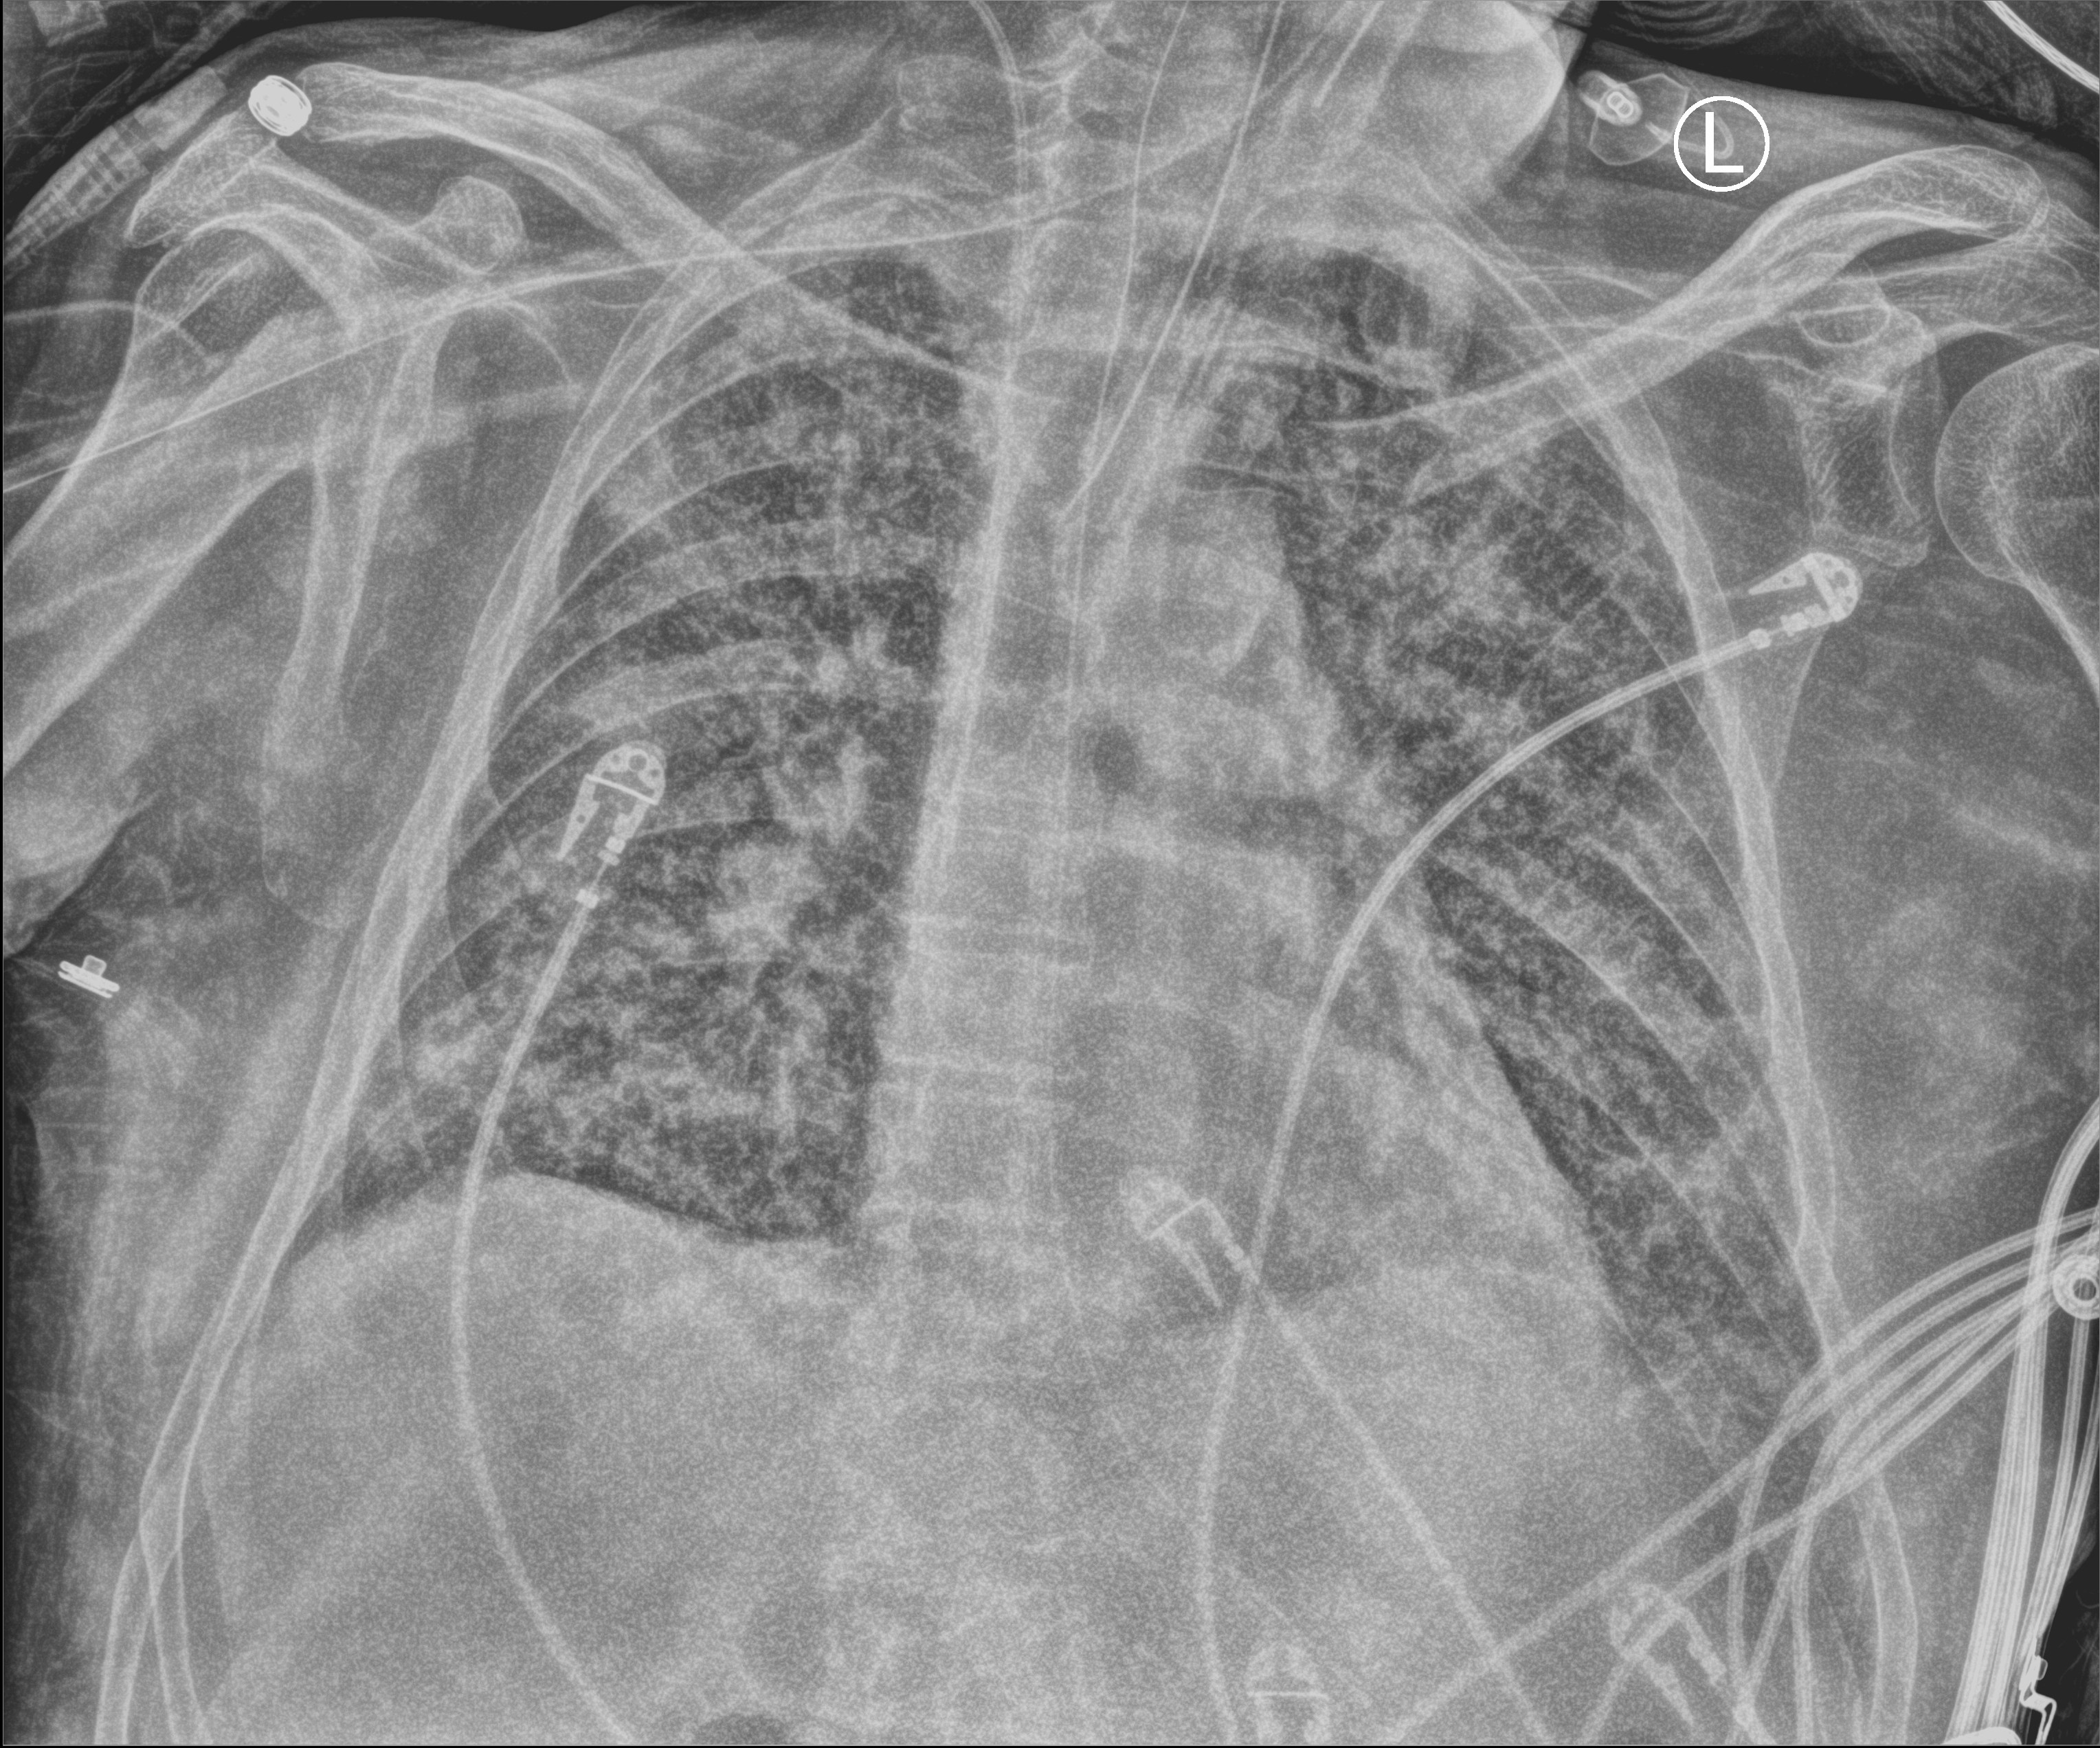
Bedside chest radiograph (computed radiography); anteroposterior (AP) projection. Patient hospitalised with COVID-19; male, aged 60–74 years.
Hospital-stay facts (about this admission, not read from this image; timing relative to this image not recorded):
- mechanically ventilated during this hospital stay: yes
- diabetes (admission record): no
- admitted to intensive care during this hospital stay: yes